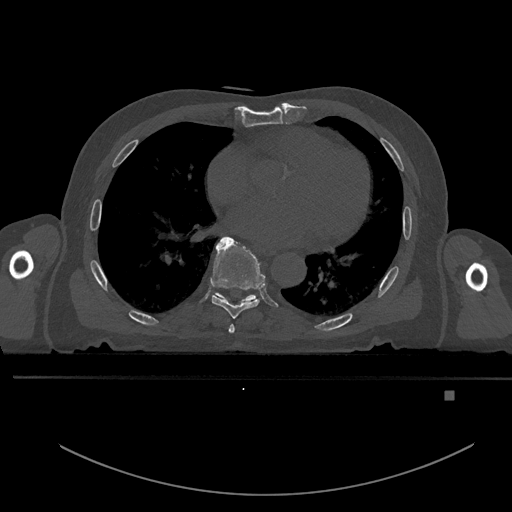
CT including the spine, one axial slice; bone window (W 1800 / L 400 HU); 0.5 mm slice thickness; 512 × 512 image matrix, field of view 456 × 456 mm. Patient: male, 82 years. From the clinical record (not read from this slice): primary cancer: prostate.
Structures marked on this image (semi-automatically segmented with operator editing):
- T6 vertebra: bounding box <229,324,235,333> (left, top, right, bottom; pixels)
- T7 vertebra: <211,237,265,319>
- T8 vertebra: <212,293,258,304>